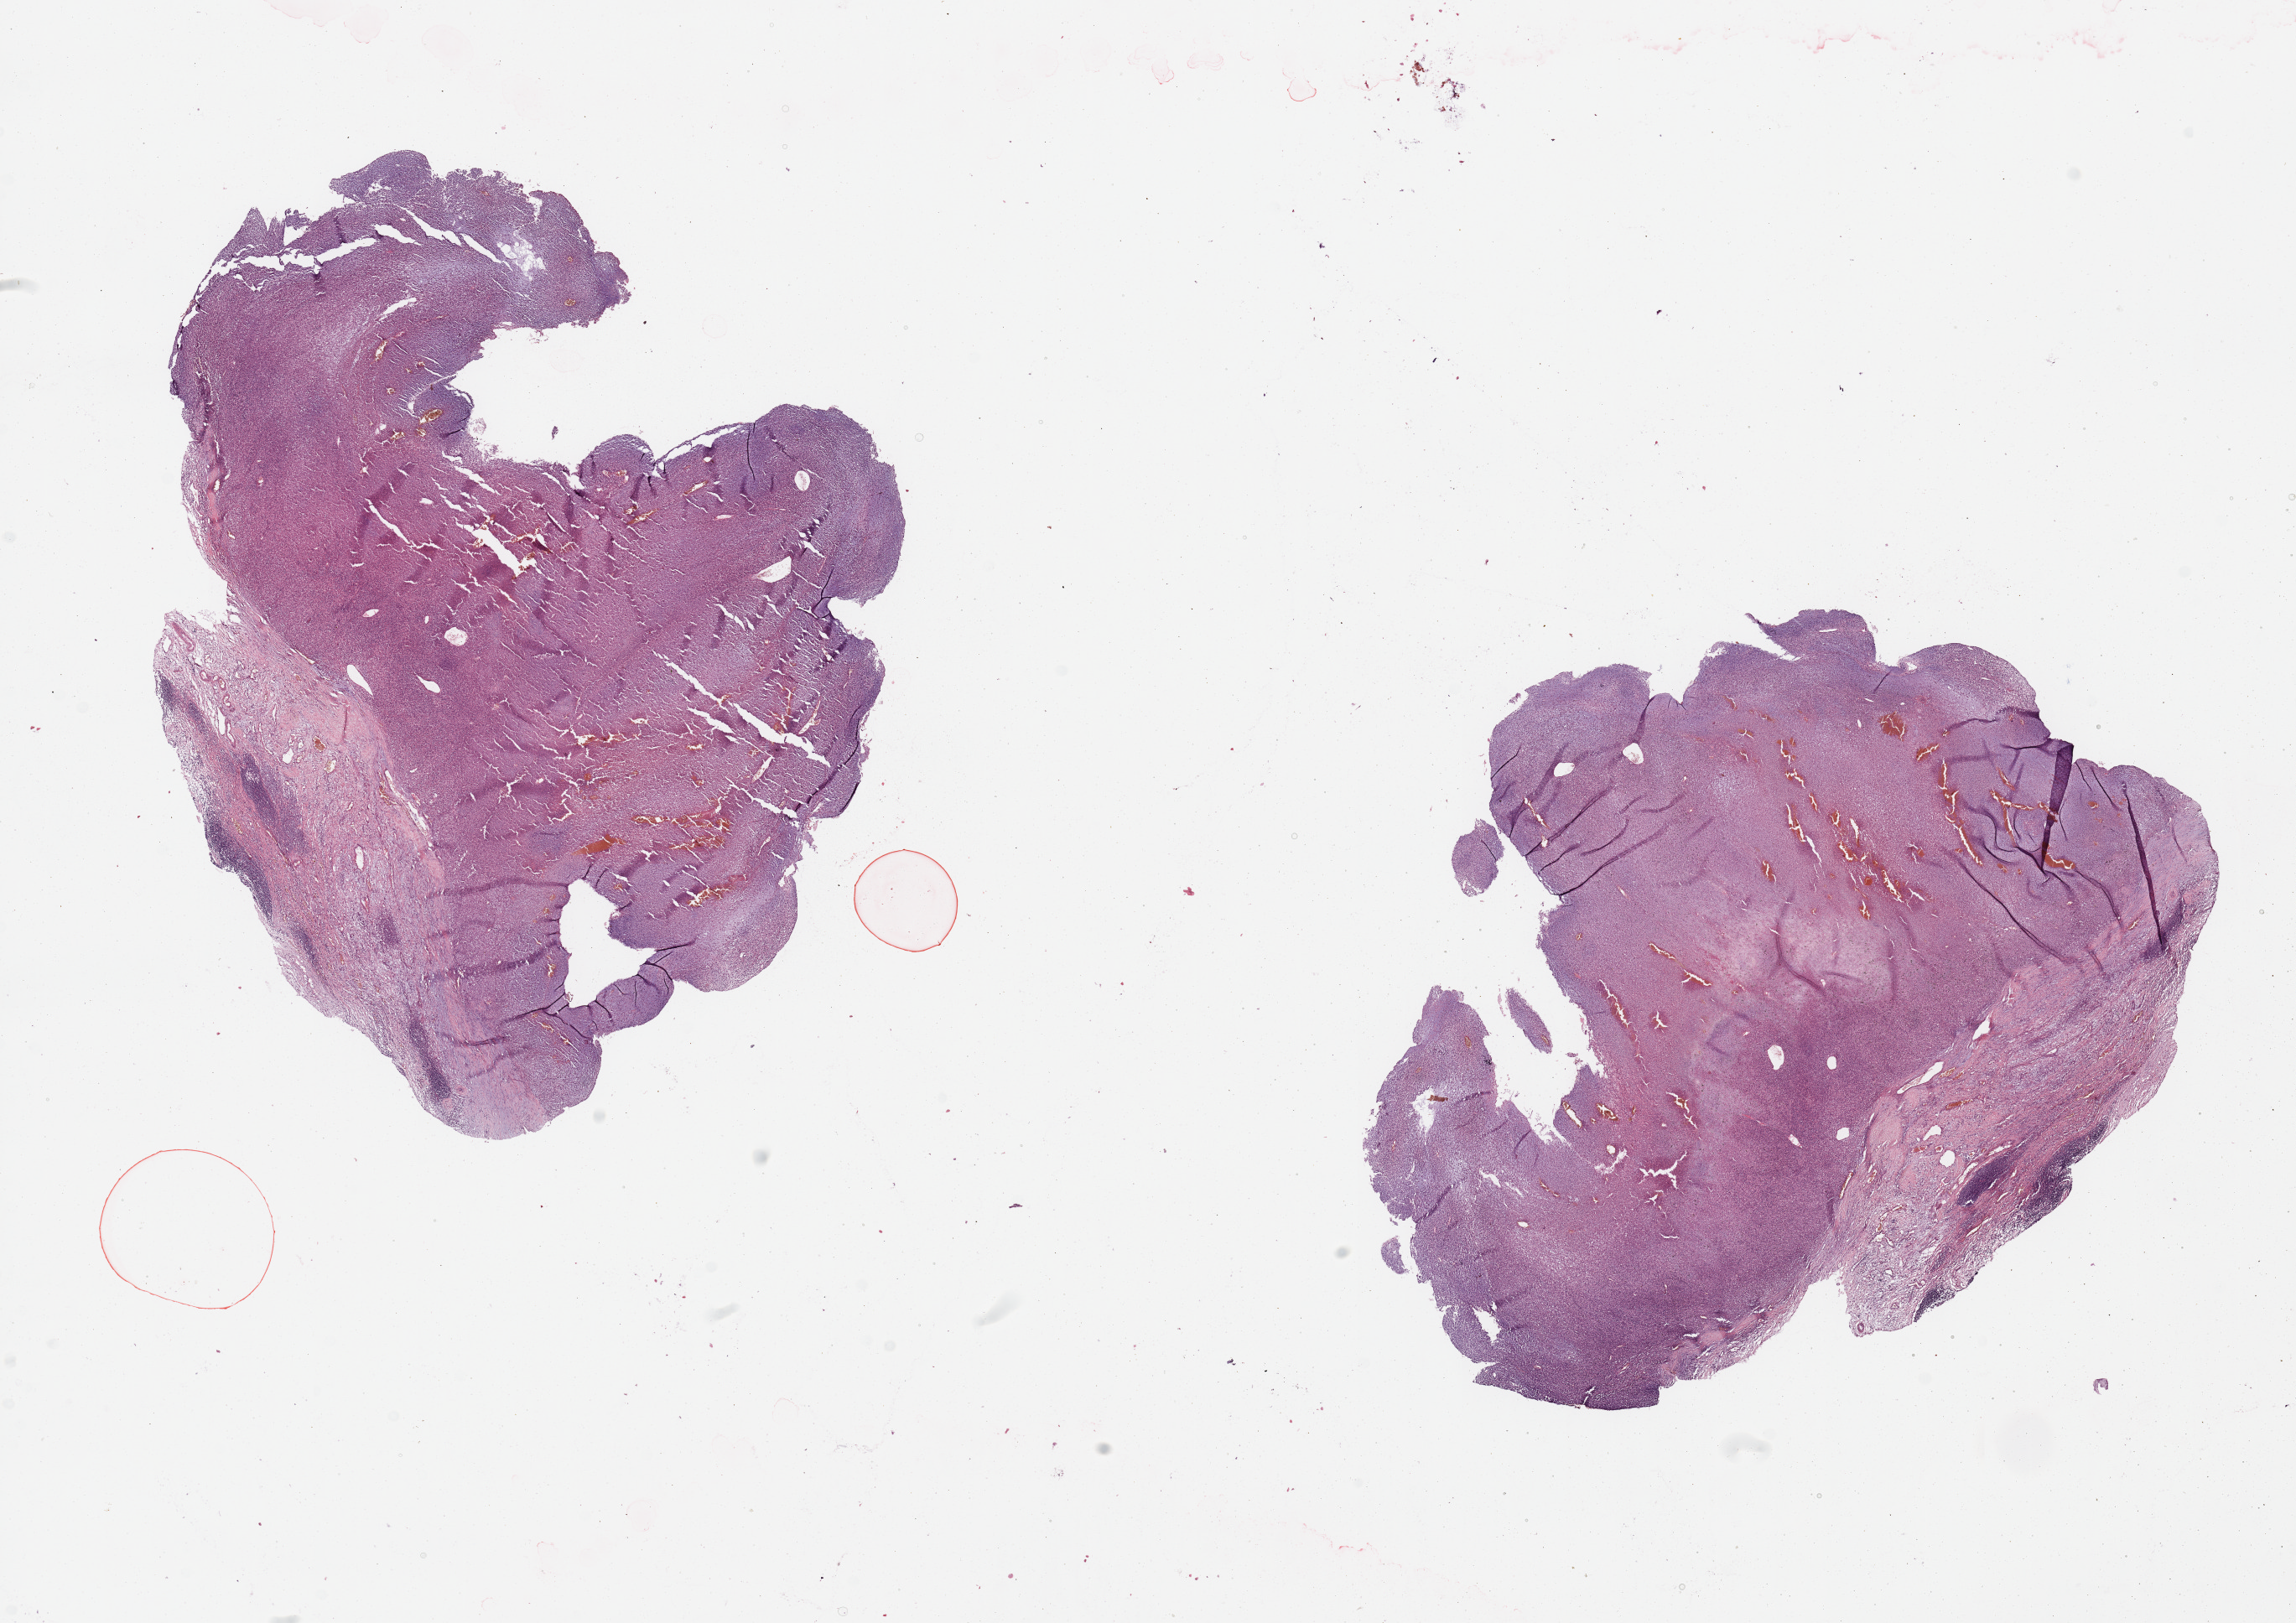
Whole-slide histology image, H&E-stained, whole scanned area (about 21.7 x 15.3 mm) shown as a low-resolution overview; tumour tissue sample, sampled site: lymph node. Patient: female, age 68 years. Pathologist review of this section (percent, as recorded): tumour nuclei 90%, necrosis 2%.
This section: metastatic tumour tissue. Primary tumour site (as recorded): extremities. Patient diagnosis: Malignant melanoma, NOS.